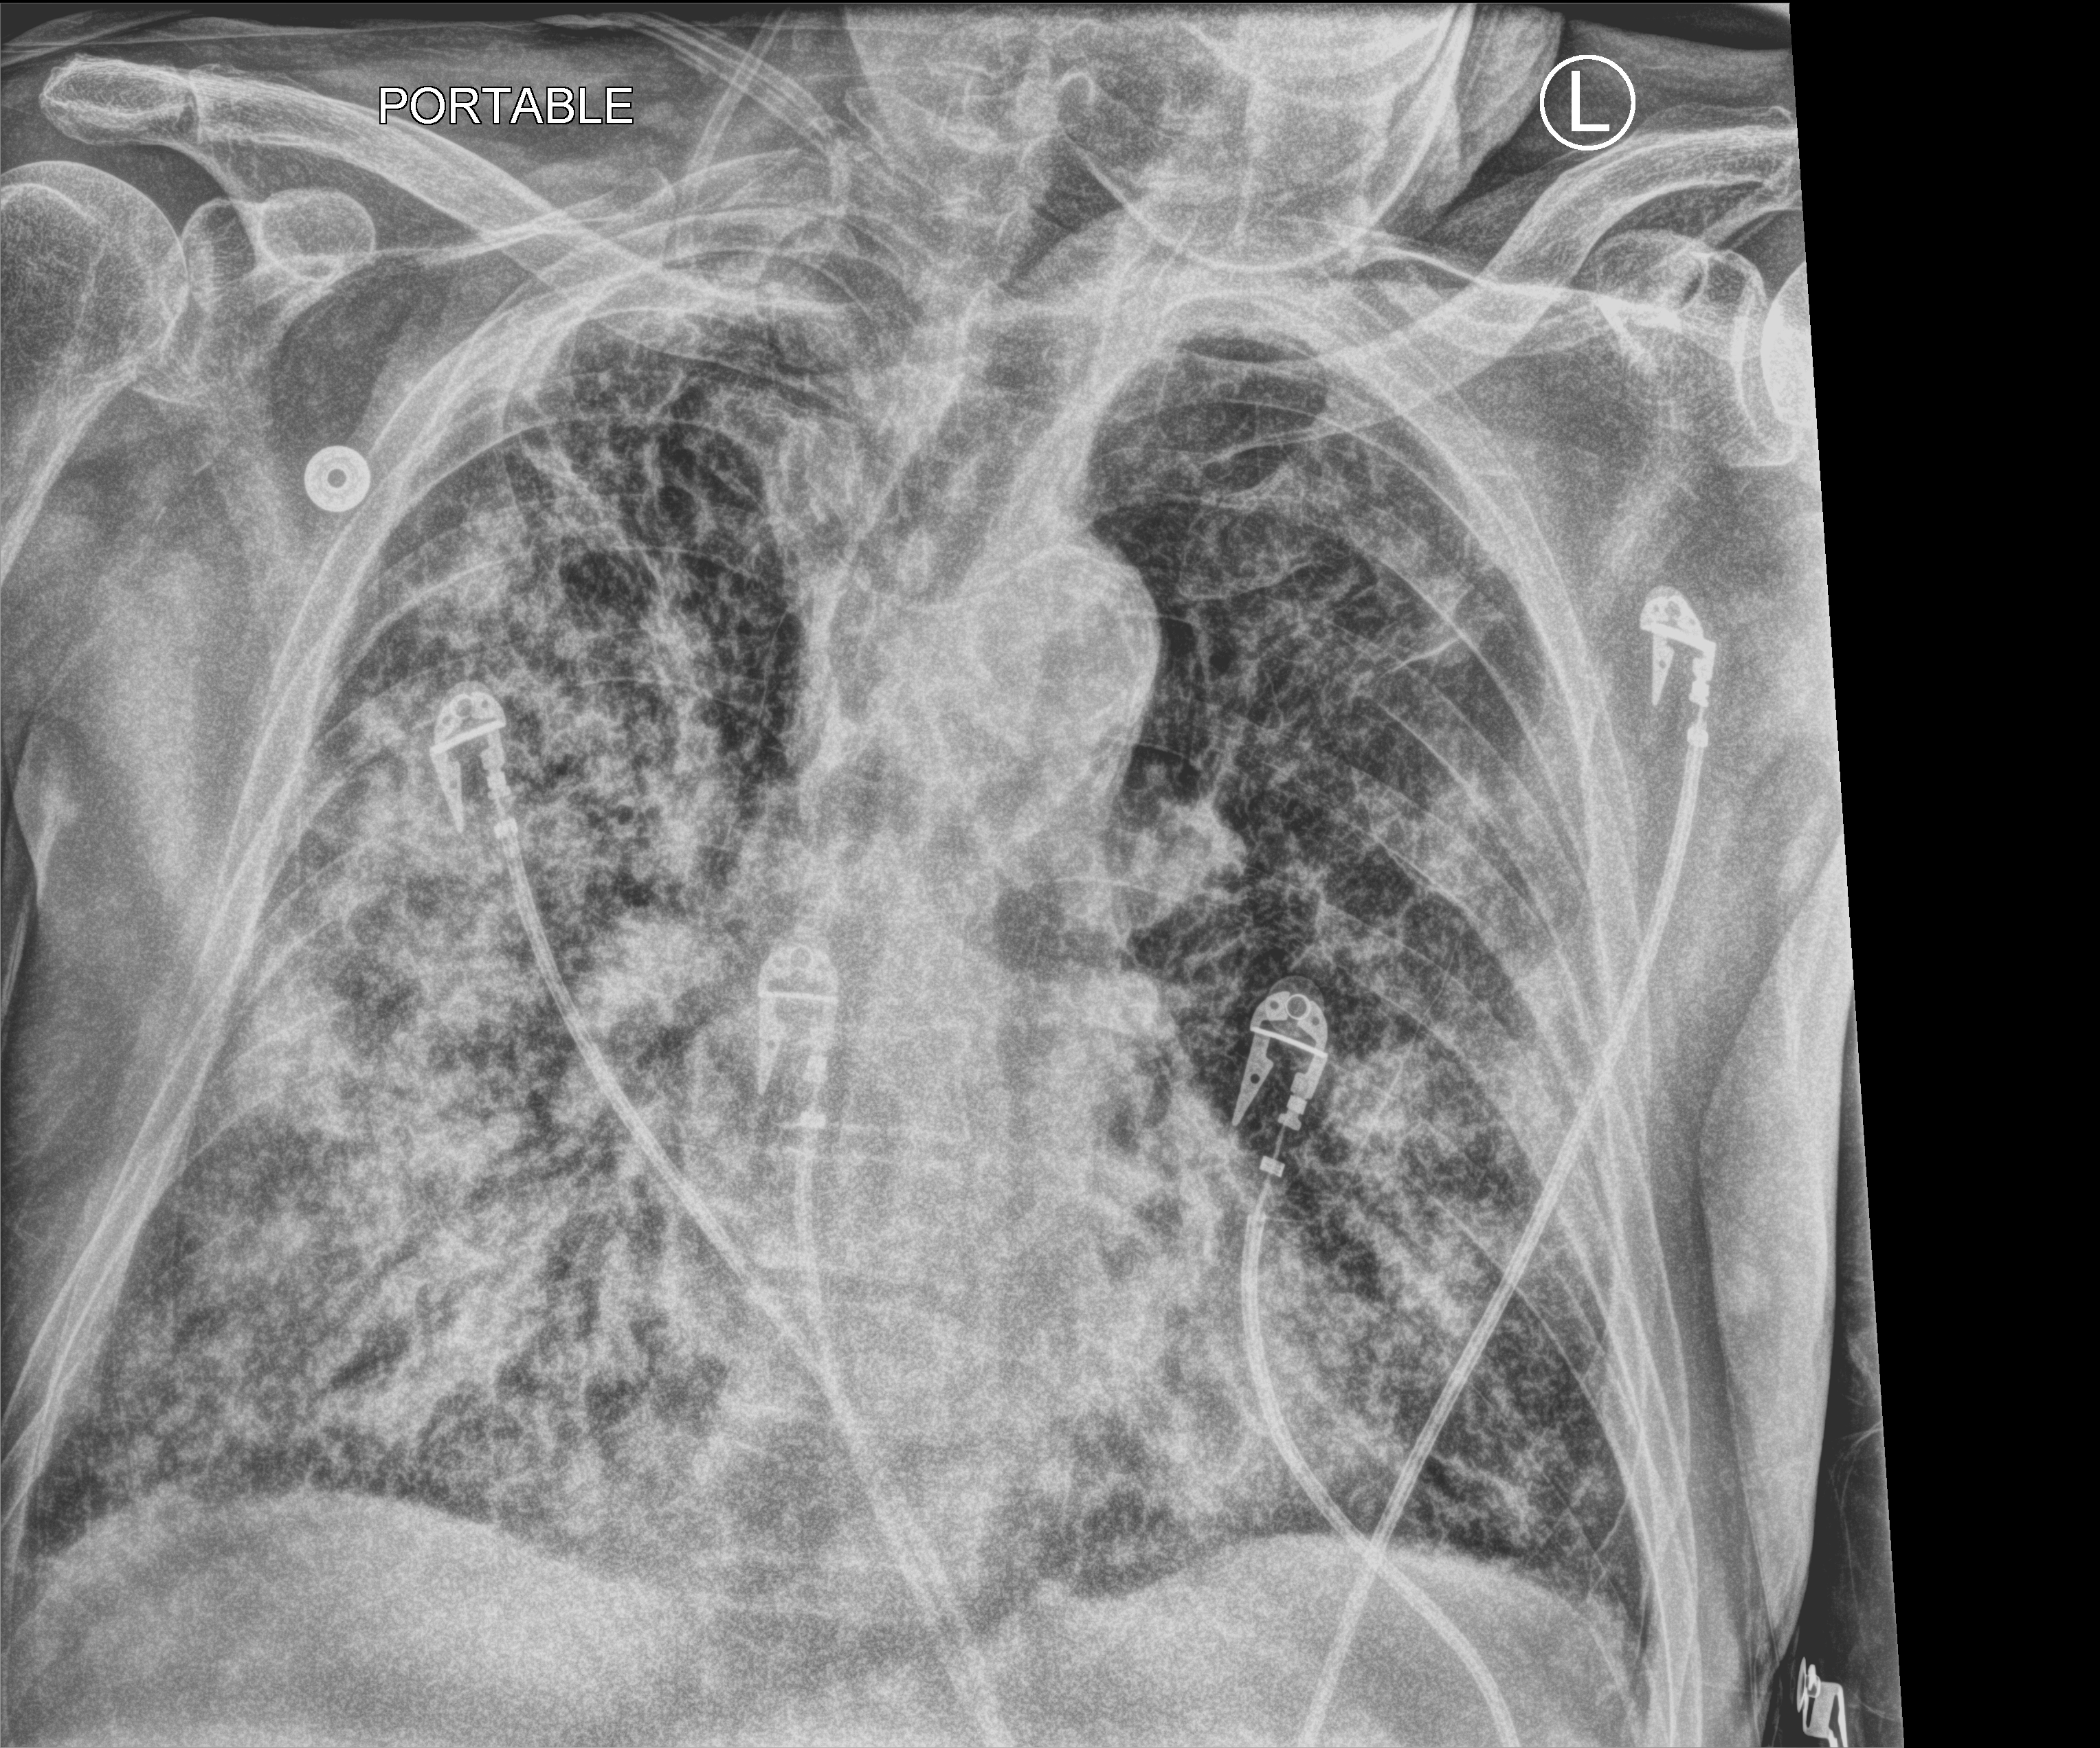
Portable chest radiograph, anteroposterior (AP) projection. Male patient hospitalised with COVID-19, age 75–90 years.
From the hospital-stay record, not from the radiograph (when in the stay this image was taken is not recorded):
- mechanically ventilated during this hospital stay: no